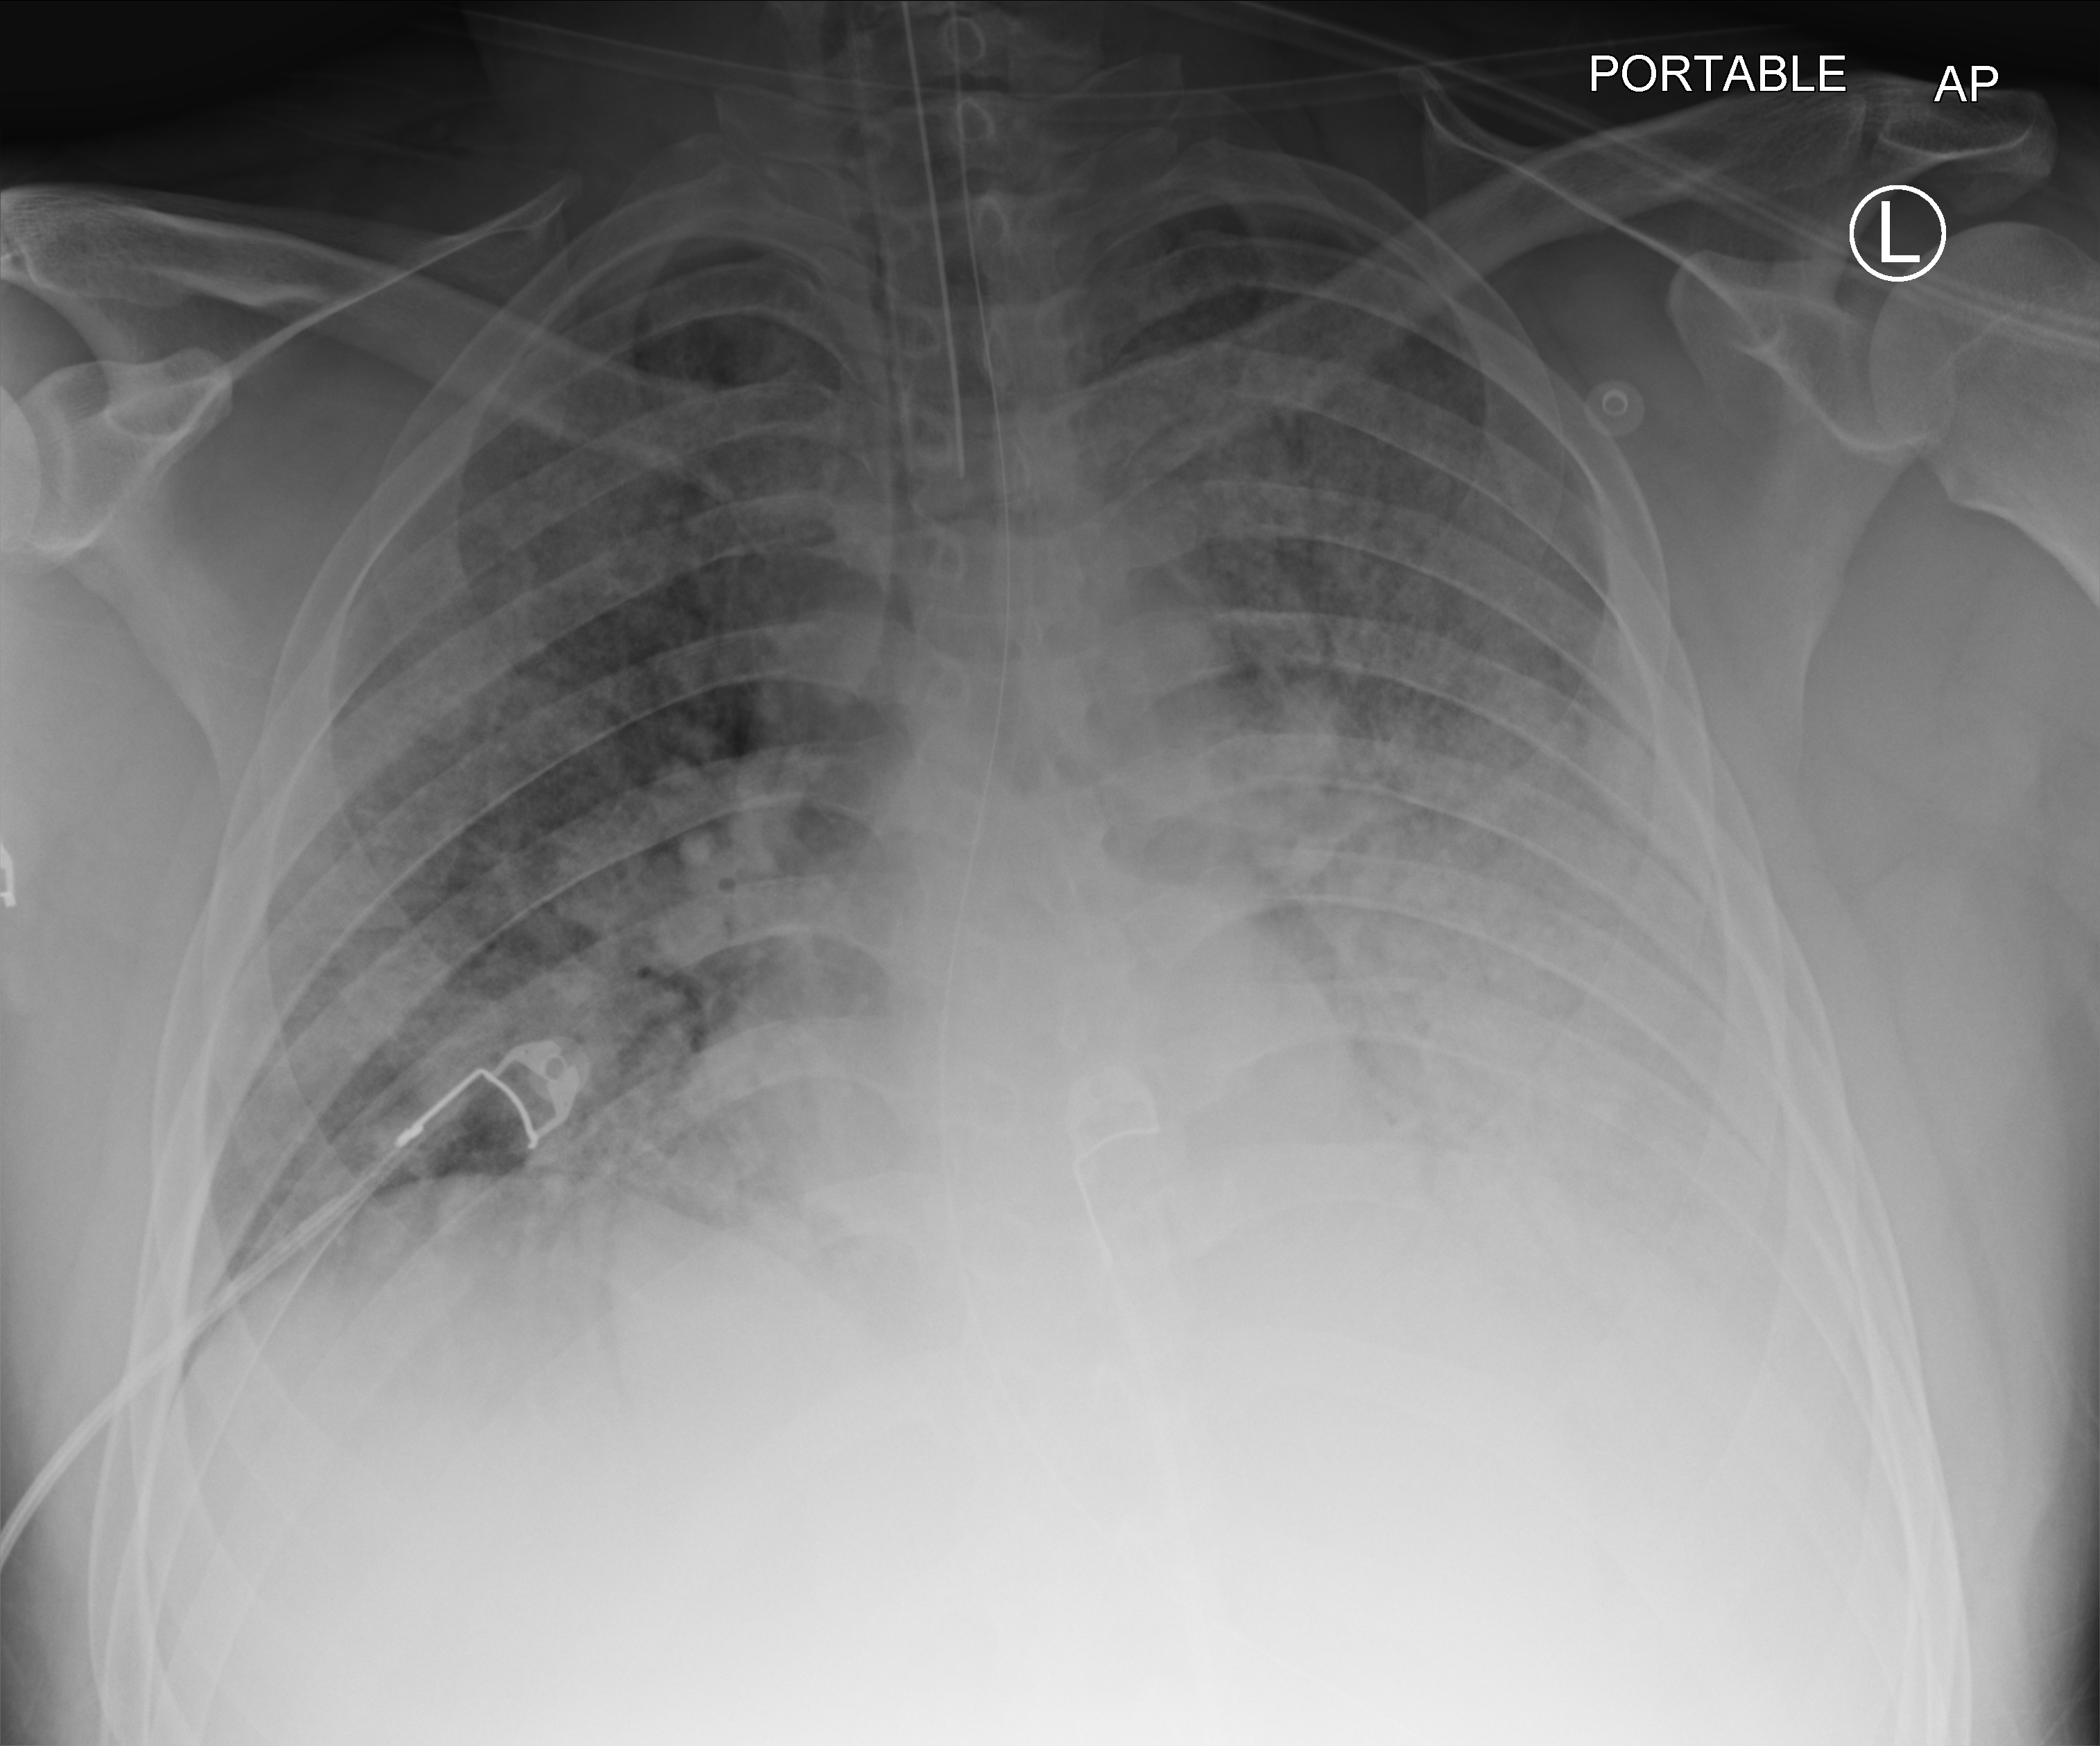
Portable chest radiograph, anteroposterior (AP) projection. Patient hospitalised with COVID-19; male, aged 18–59 years.
Admission-level facts for this patient (not findings on this image; timing relative to this image not recorded):
- hypertension (admission record): yes
- smoking status (admission record): current
- mechanically ventilated during this hospital stay: yes